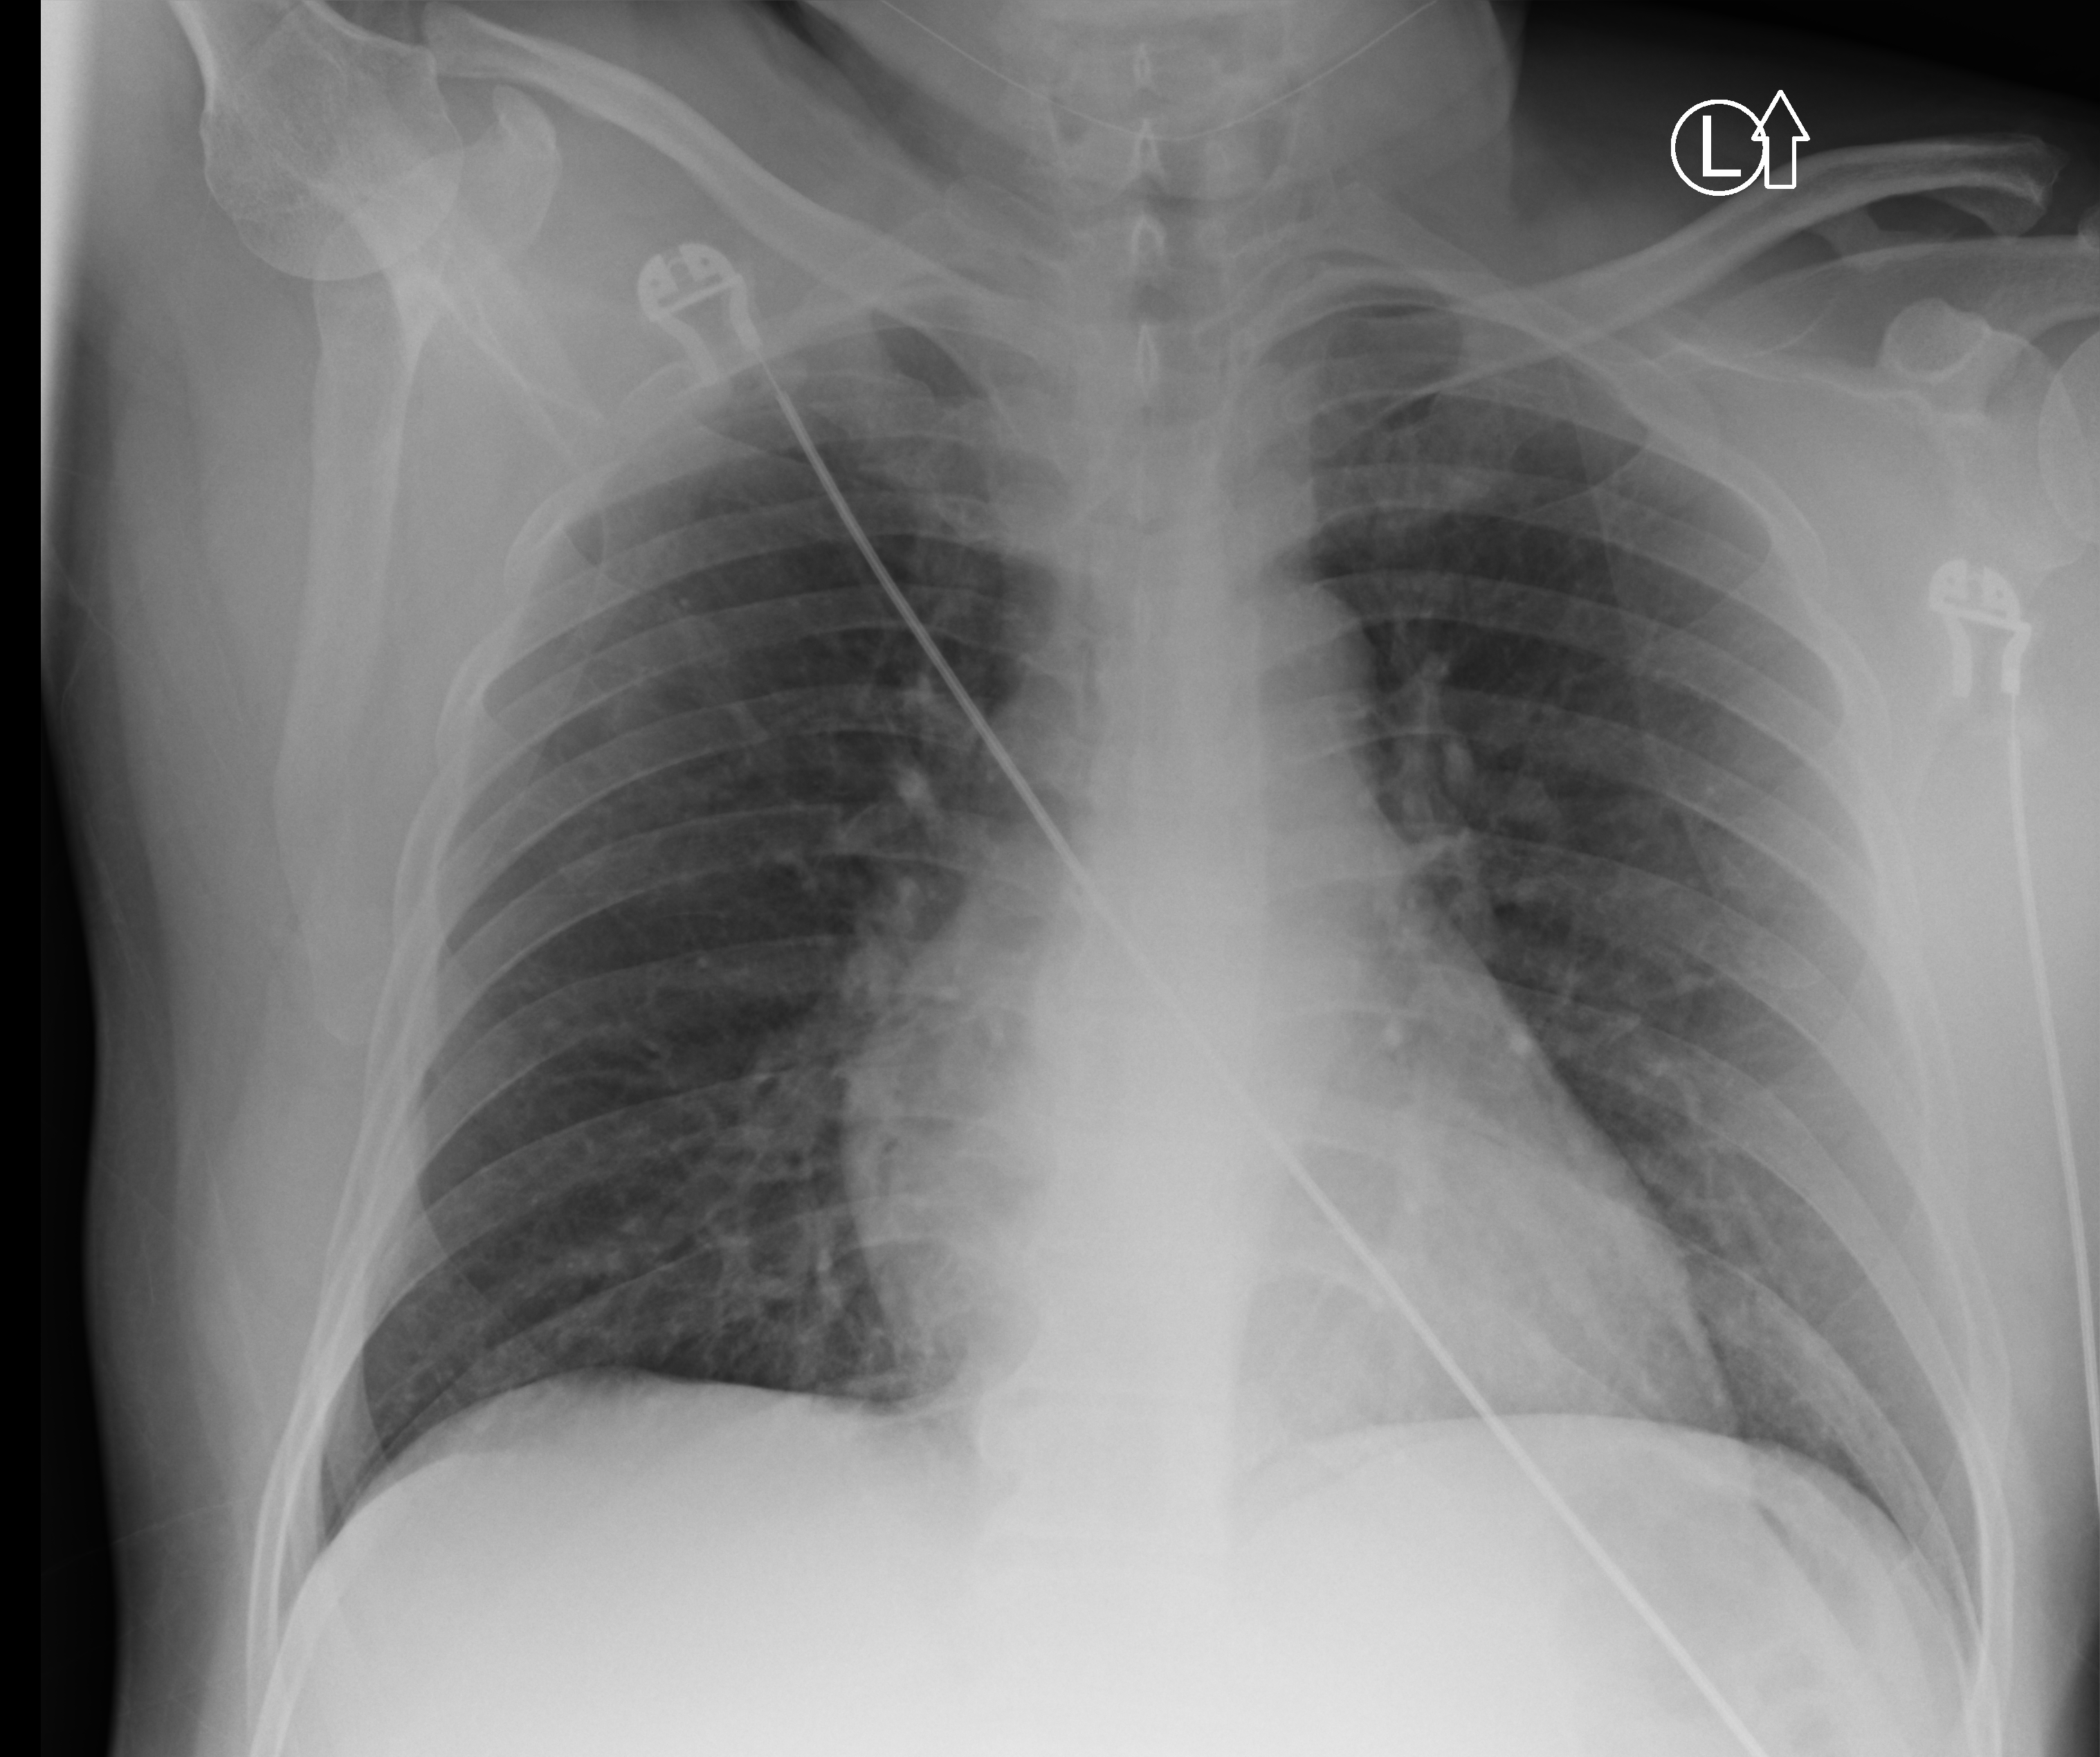
Portable chest radiograph; anteroposterior (AP) projection. Male patient hospitalised with COVID-19, age 18–59 years.
Hospital-stay facts (about this admission, not read from this image; timing relative to this image not recorded): mechanically ventilated during this hospital stay: no; admitted to intensive care during this hospital stay: no.